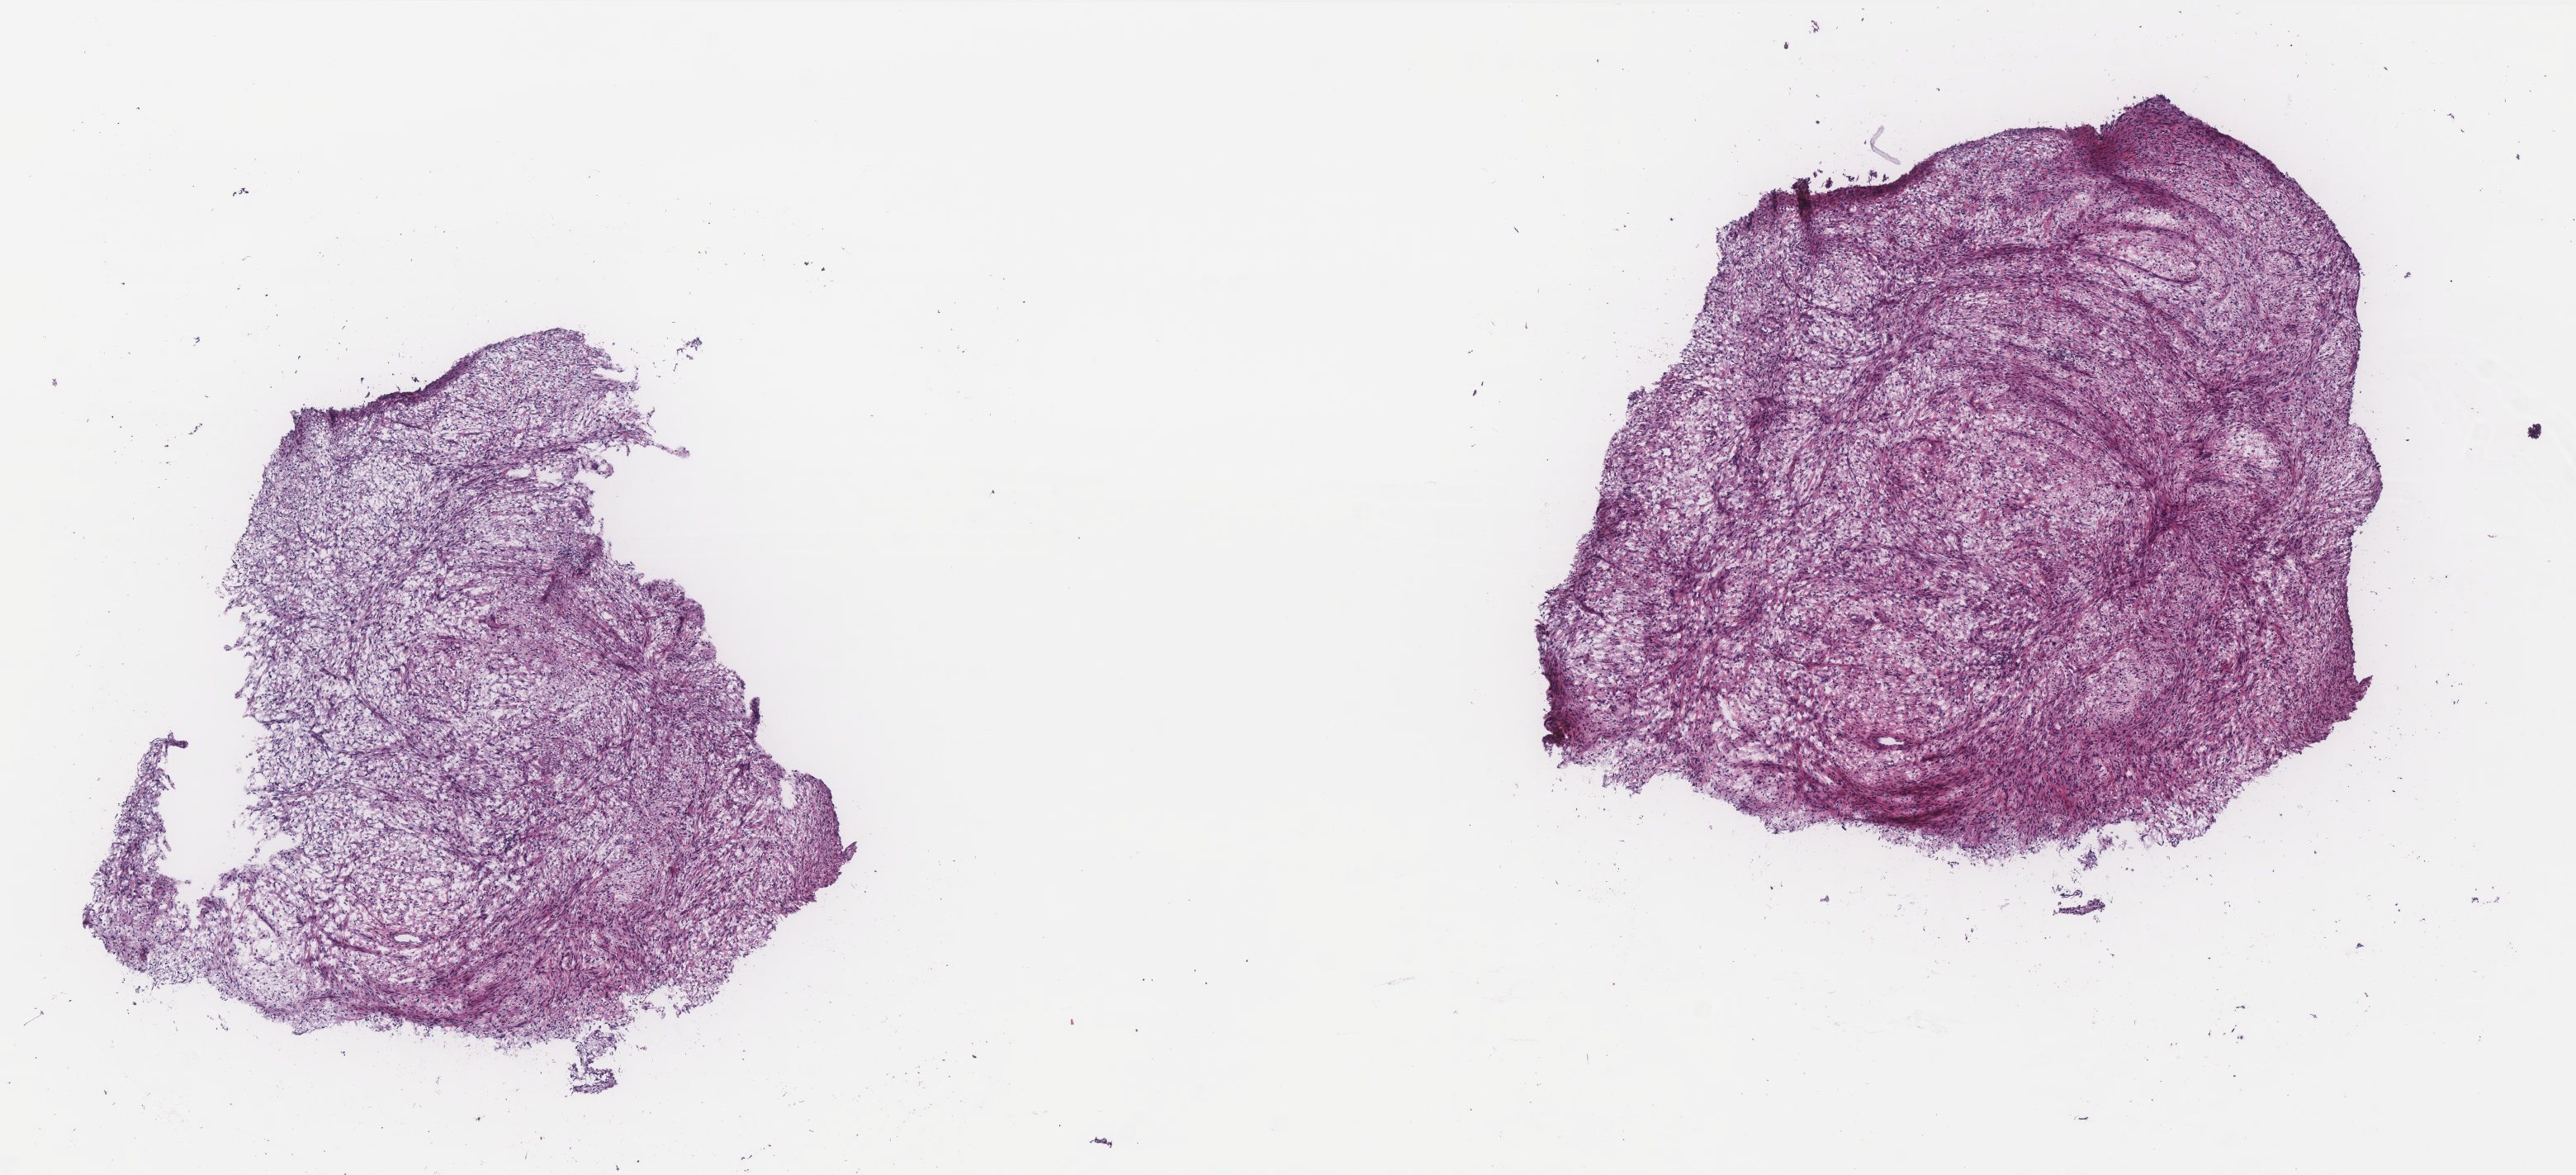
Whole-slide histology image, H&E, shown as a low-resolution overview of the whole scanned area (about 12.5 x 5.7 mm, from a 40x scan). Frozen section from the top of the tissue portion. Sample: primary tumour, retroperitoneum and peritoneum. Patient: female, age at initial diagnosis 60 years. Composition of this section per pathologist review: tumour cells 85%, tumour nuclei 85%, normal cells 0%, stromal cells 15%, necrosis 0%. Inflammatory infiltration, as recorded: lymphocyte infiltration 2%, monocyte infiltration 1%, neutrophil infiltration 1%.
Pathologic diagnosis: Dedifferentiated liposarcoma.